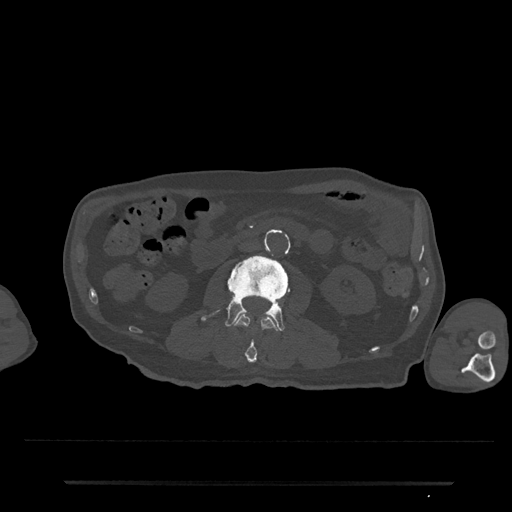
CT including the spine, one axial slice. Position 16 of 797 along the scan axis. 120 kVp. Bone window (W 1800 / L 400 HU). 0.5 mm slice thickness. 512 × 512 image matrix, field of view 427 × 427 mm. Patient: male, 74 years. Case-level facts recorded for this patient, not image findings: primary cancer: prostate.
Structures marked on this image (semi-automatically segmented with operator editing):
- L2 vertebra: bounding box <234,314,278,363> (left, top, right, bottom; pixels)
- L3 vertebra: <201,255,290,331>